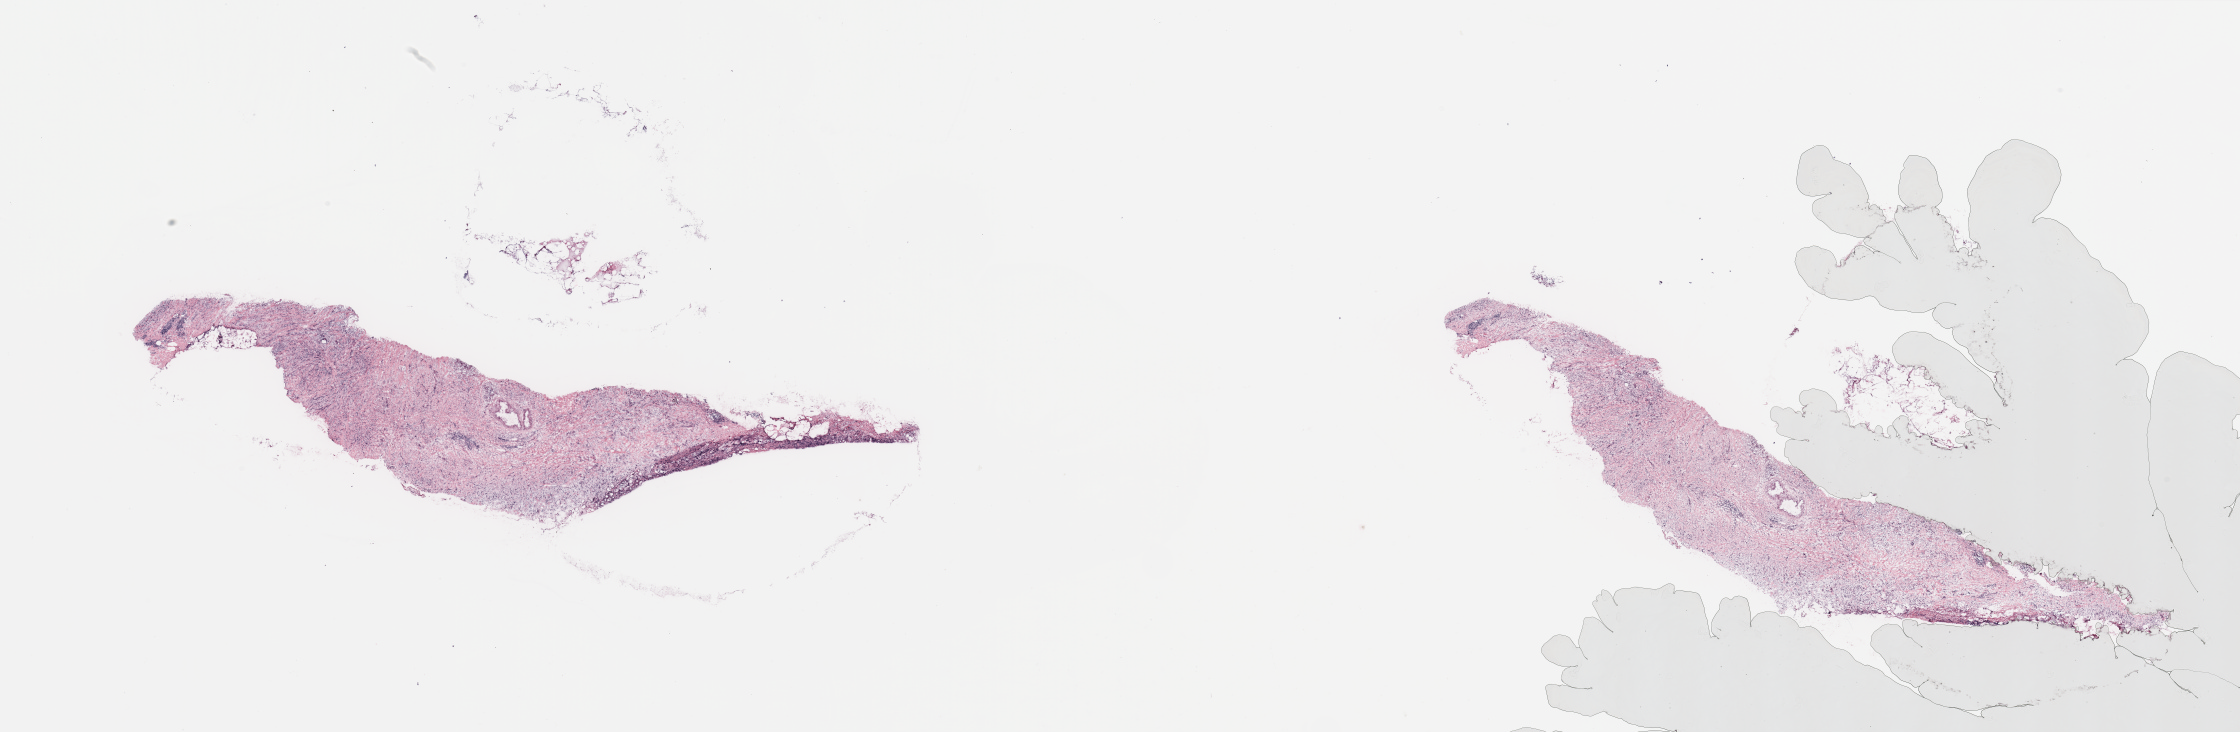
Digitized Hematoxylin and eosin (H&E) stained tissue section (whole slide), low-resolution overview of the scanned area, about 35.4 x 11.6 mm (from a 20x scan). Breast, tissue type not recorded.
Patient diagnosis (cohort enrolment): breast cancer (breast).